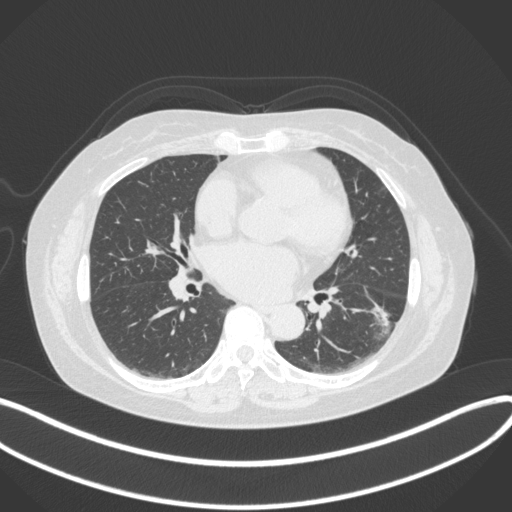
Chest CT, one axial slice; position 170 of 373 along the scan axis; 120 kVp; lung window (W 1500 / L -600 HU); 1 mm slice thickness; 512 × 512 image matrix, field of view 400 × 400 mm. Female patient, age 67 years. From the clinical record (not read from this slice): clinical TNM (as recorded): T1c N0 M0; histopathological grade: G2.
Structures marked on this image (bounding box drawn by a radiologist):
- lung tumour (recorded histology: adenocarcinoma): bounding box (x1, y1, x2, y2) in pixels: (362, 299, 395, 333)